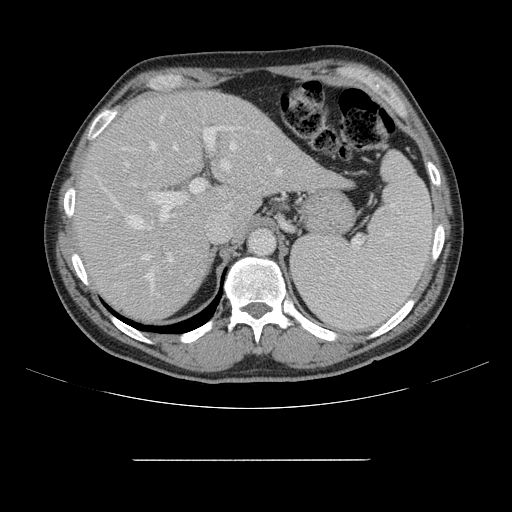
Contrast-enhanced abdominal CT, one axial slice; position 107 of 164 along the scan axis; intravenous contrast given; soft-tissue window (W 400 / L 40 HU); 2.5 mm slice thickness; 512 × 512 image matrix, field of view 404 × 404 mm. Male patient, age 54 years. Case-level facts recorded for this patient, not image findings: diagnosis: colorectal cancer liver metastases, imaged before liver resection; multiple liver metastases: yes; largest metastasis: 1 cm; disease in both lobes: no.
Outlined on this slice (manually delineated by an expert):
- hepatic veins: box from (x=100, y=117) to (x=282, y=278) px
- liver: (x=76, y=92)–(x=344, y=321)
- planned liver remnant (the part of the liver to remain after resection): (x=77, y=92)–(x=240, y=321)
- portal vein (with intrahepatic branches): (x=121, y=114)–(x=232, y=297)